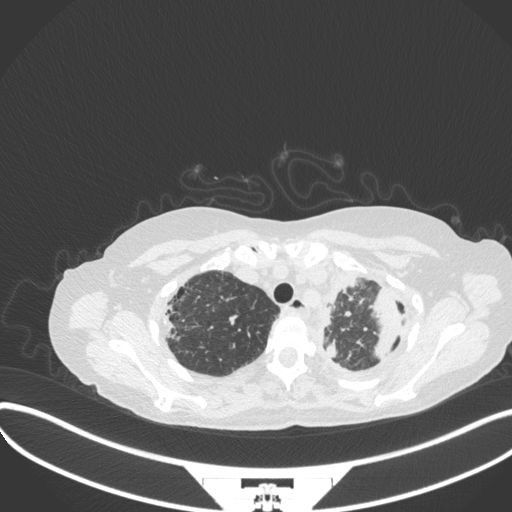
Chest CT, one axial slice; slice 285 of 373 in the series (ordered by position); reconstruction kernel B31f; 120 kVp; lung window (W 1500 / L -600 HU); 1 mm slice thickness; 512 × 512 image matrix. Female patient, age 56 years. Case-level facts recorded for this patient, not image findings: clinical TNM (as recorded): T1 N0 M0.
Annotated regions visible in this slice (rectangle marked by the reading radiologist):
- lung tumour (recorded histology: adenocarcinoma): bounding box <370,280,401,363> (left, top, right, bottom; pixels)